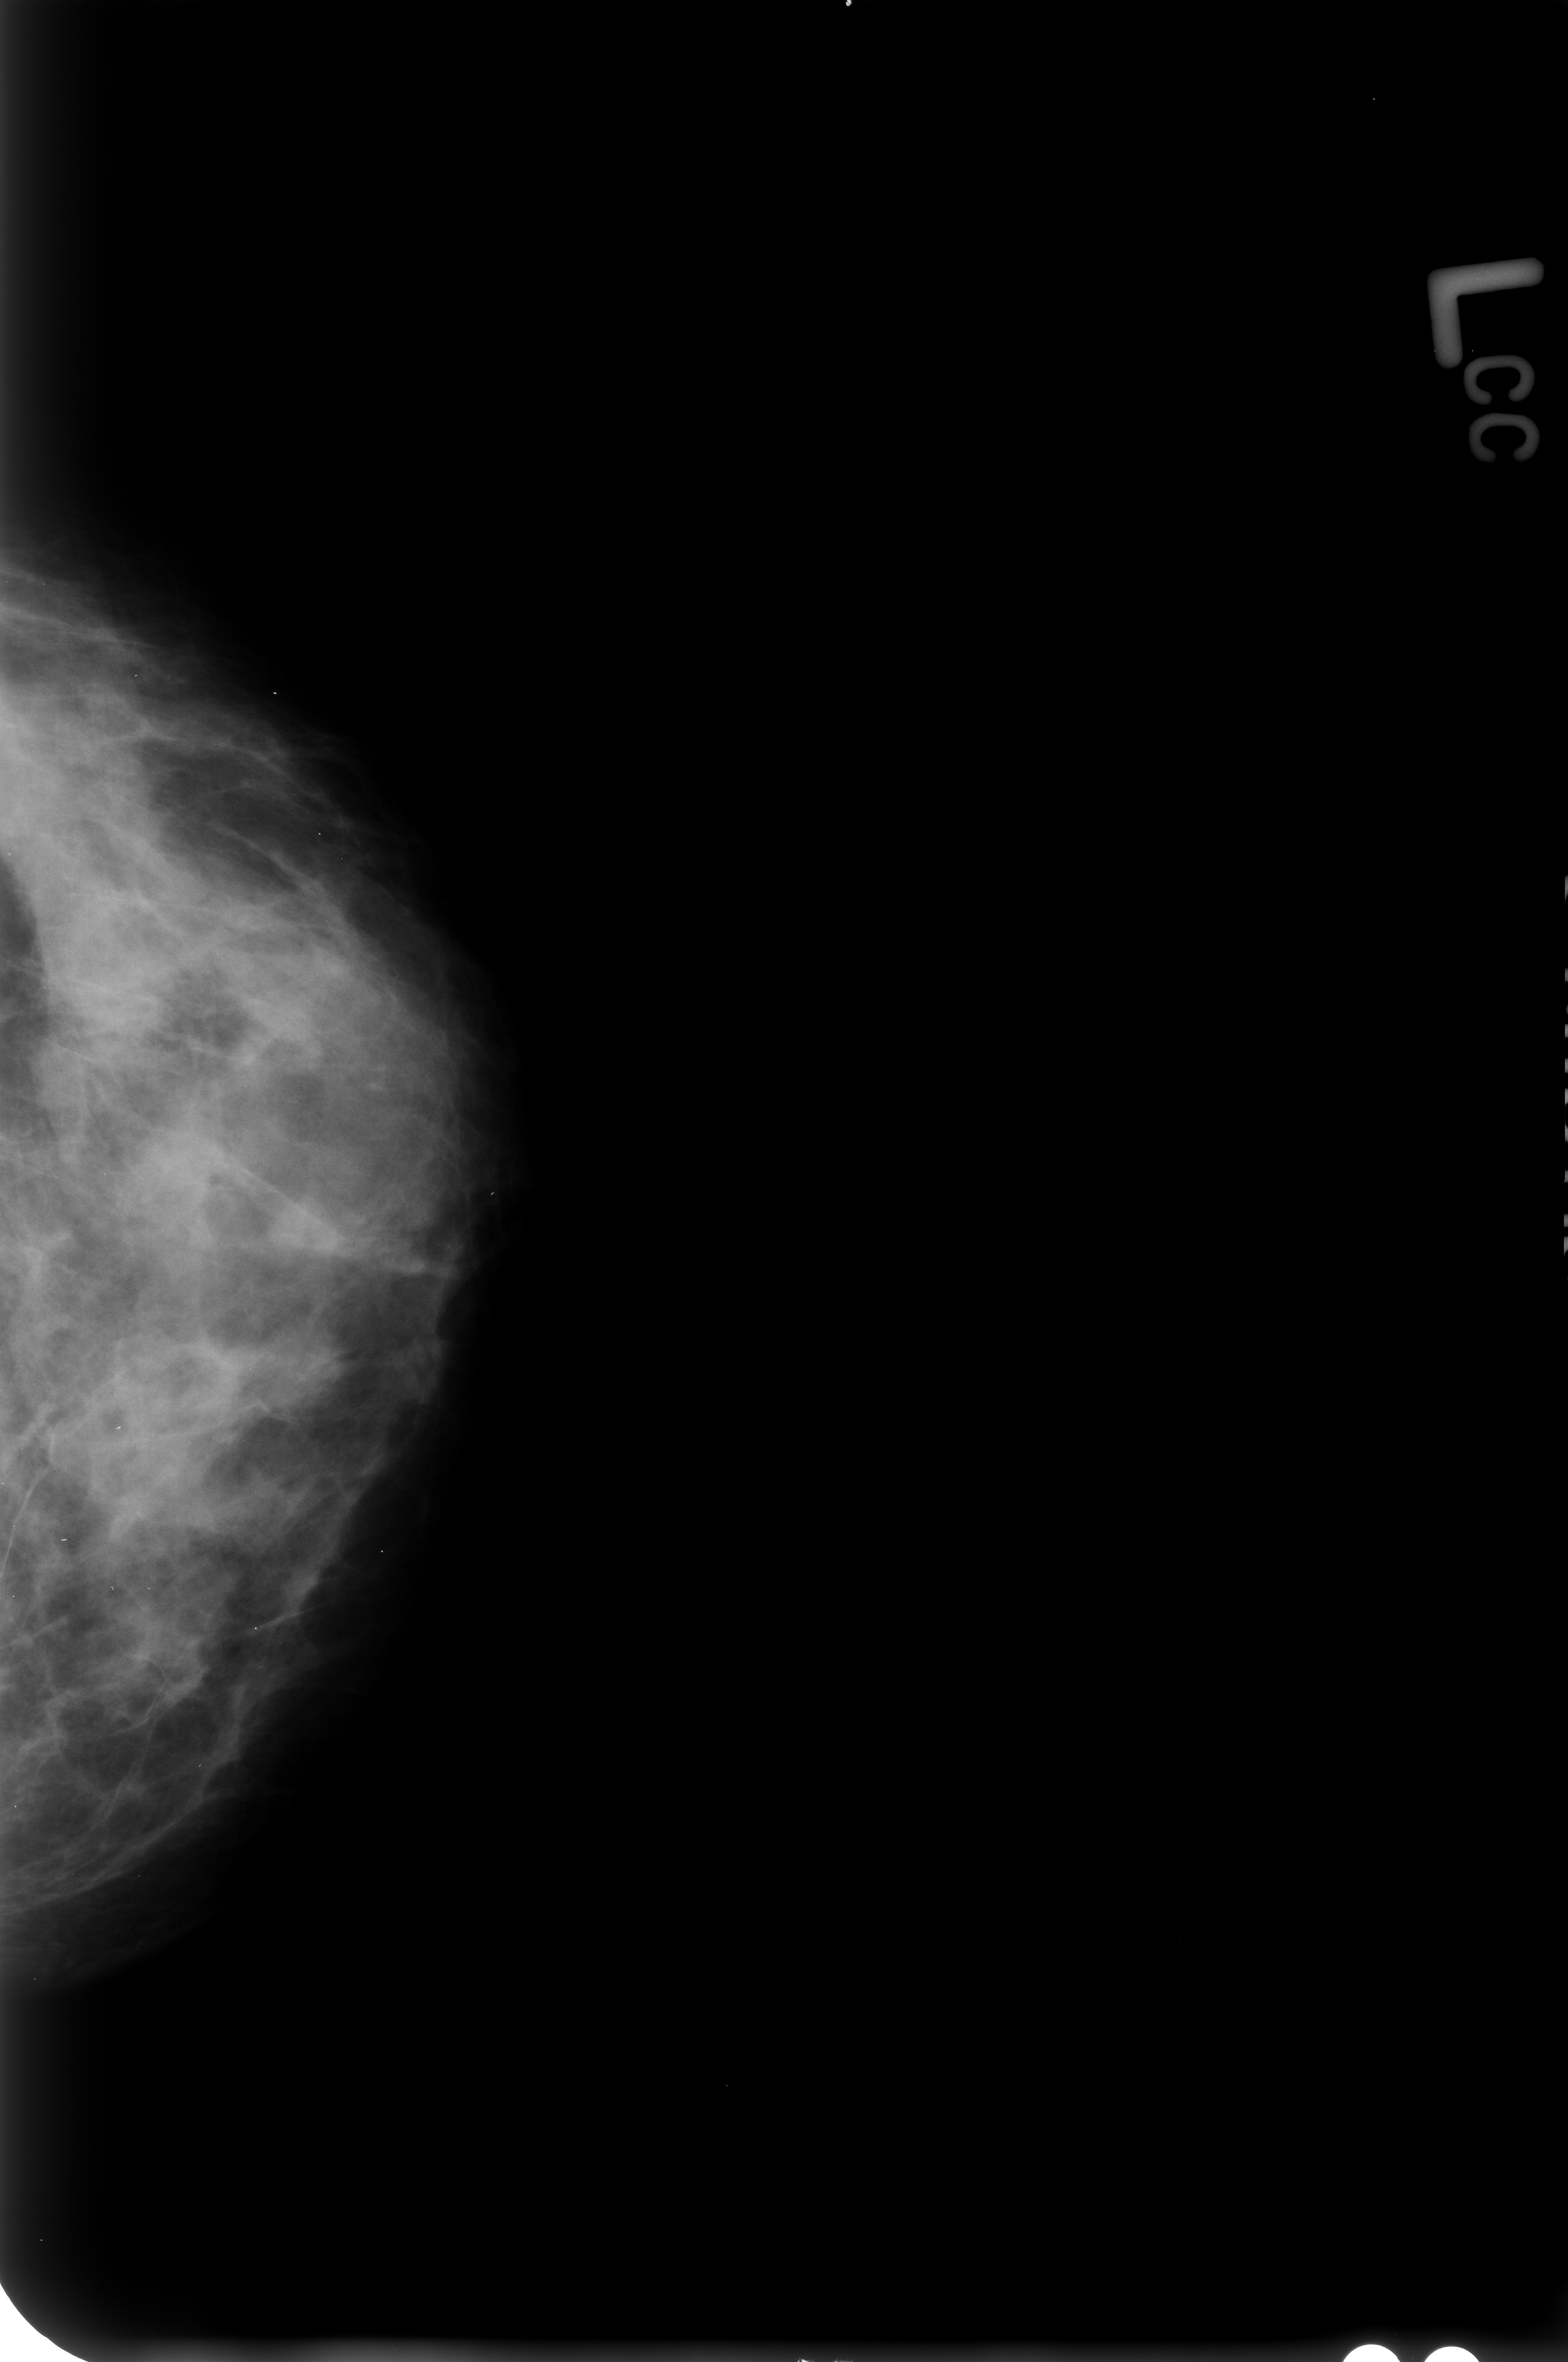
Scanned film-screen mammogram. Left breast. CC view. Breast composition: heterogeneously dense (BI-RADS density category 3 of 4). 1568 × 2362 image matrix.
Expert-marked regions of interest on this image (one box per marked abnormality):
- calcifications, morphology punctate; BI-RADS assessment category 2; outcome (as recorded, no biopsy): benign without callback (not worked up further): box from (x=0, y=830) to (x=30, y=893) px